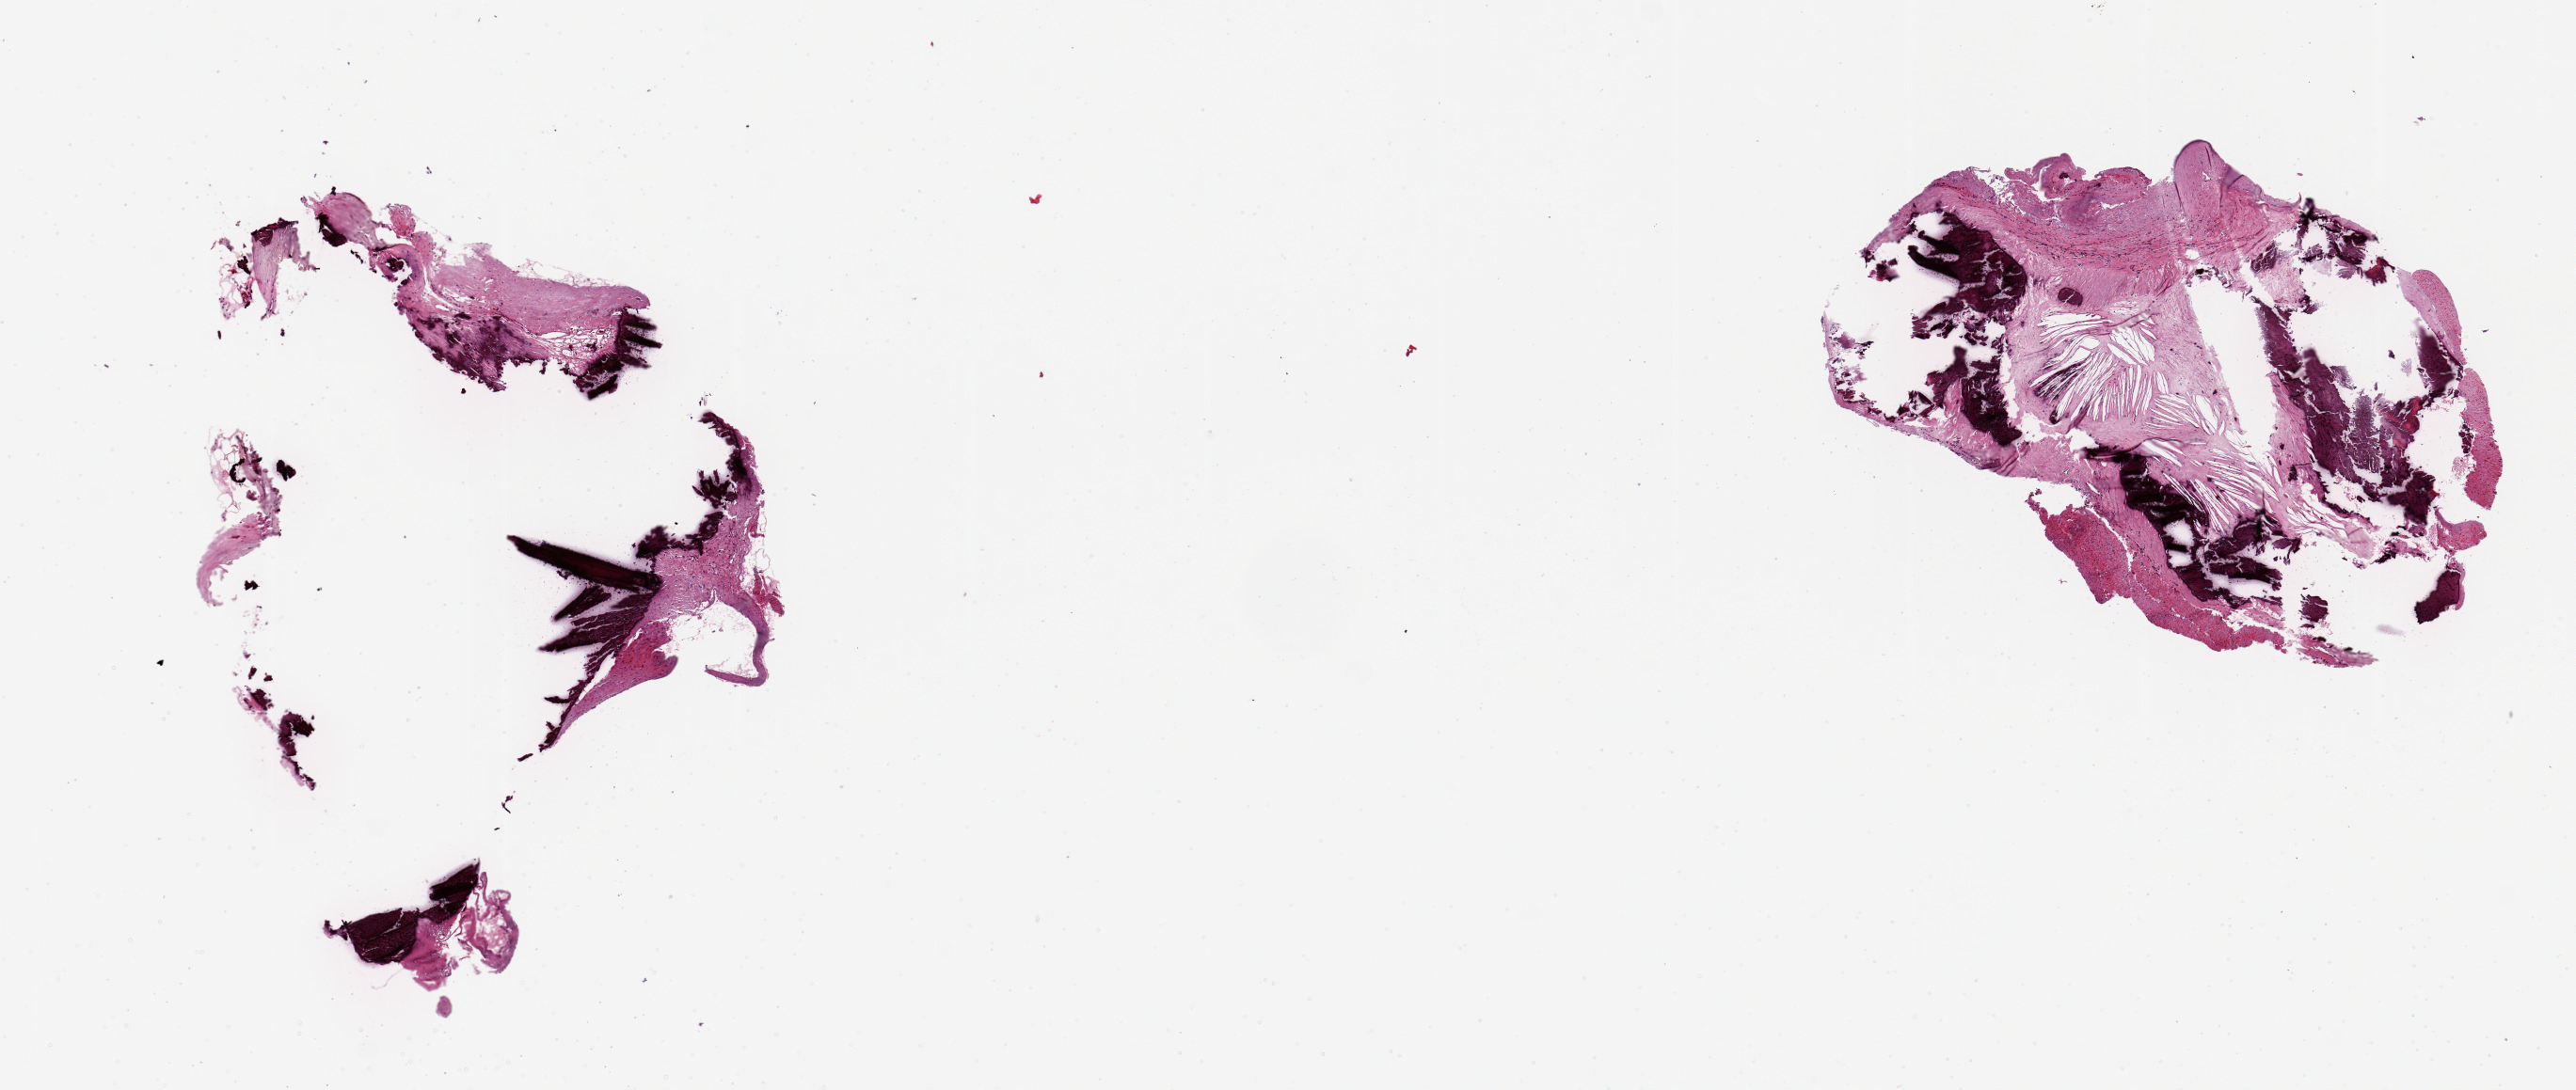
Whole-slide image, hematoxylin and eosin (H&E) stain, a low-resolution overview of the entire scanned area, about 10.8 x 4.6 mm; PAXgene-fixed, paraffin-embedded tissue; sampled site (target tissue): coronary artery; tissue donor sample. Male donor.
• pathologist's review note for this sample: 2 pieces, 3.5x3 & 3x2mm; severe atheromatous and calcific changes; no normal tissue